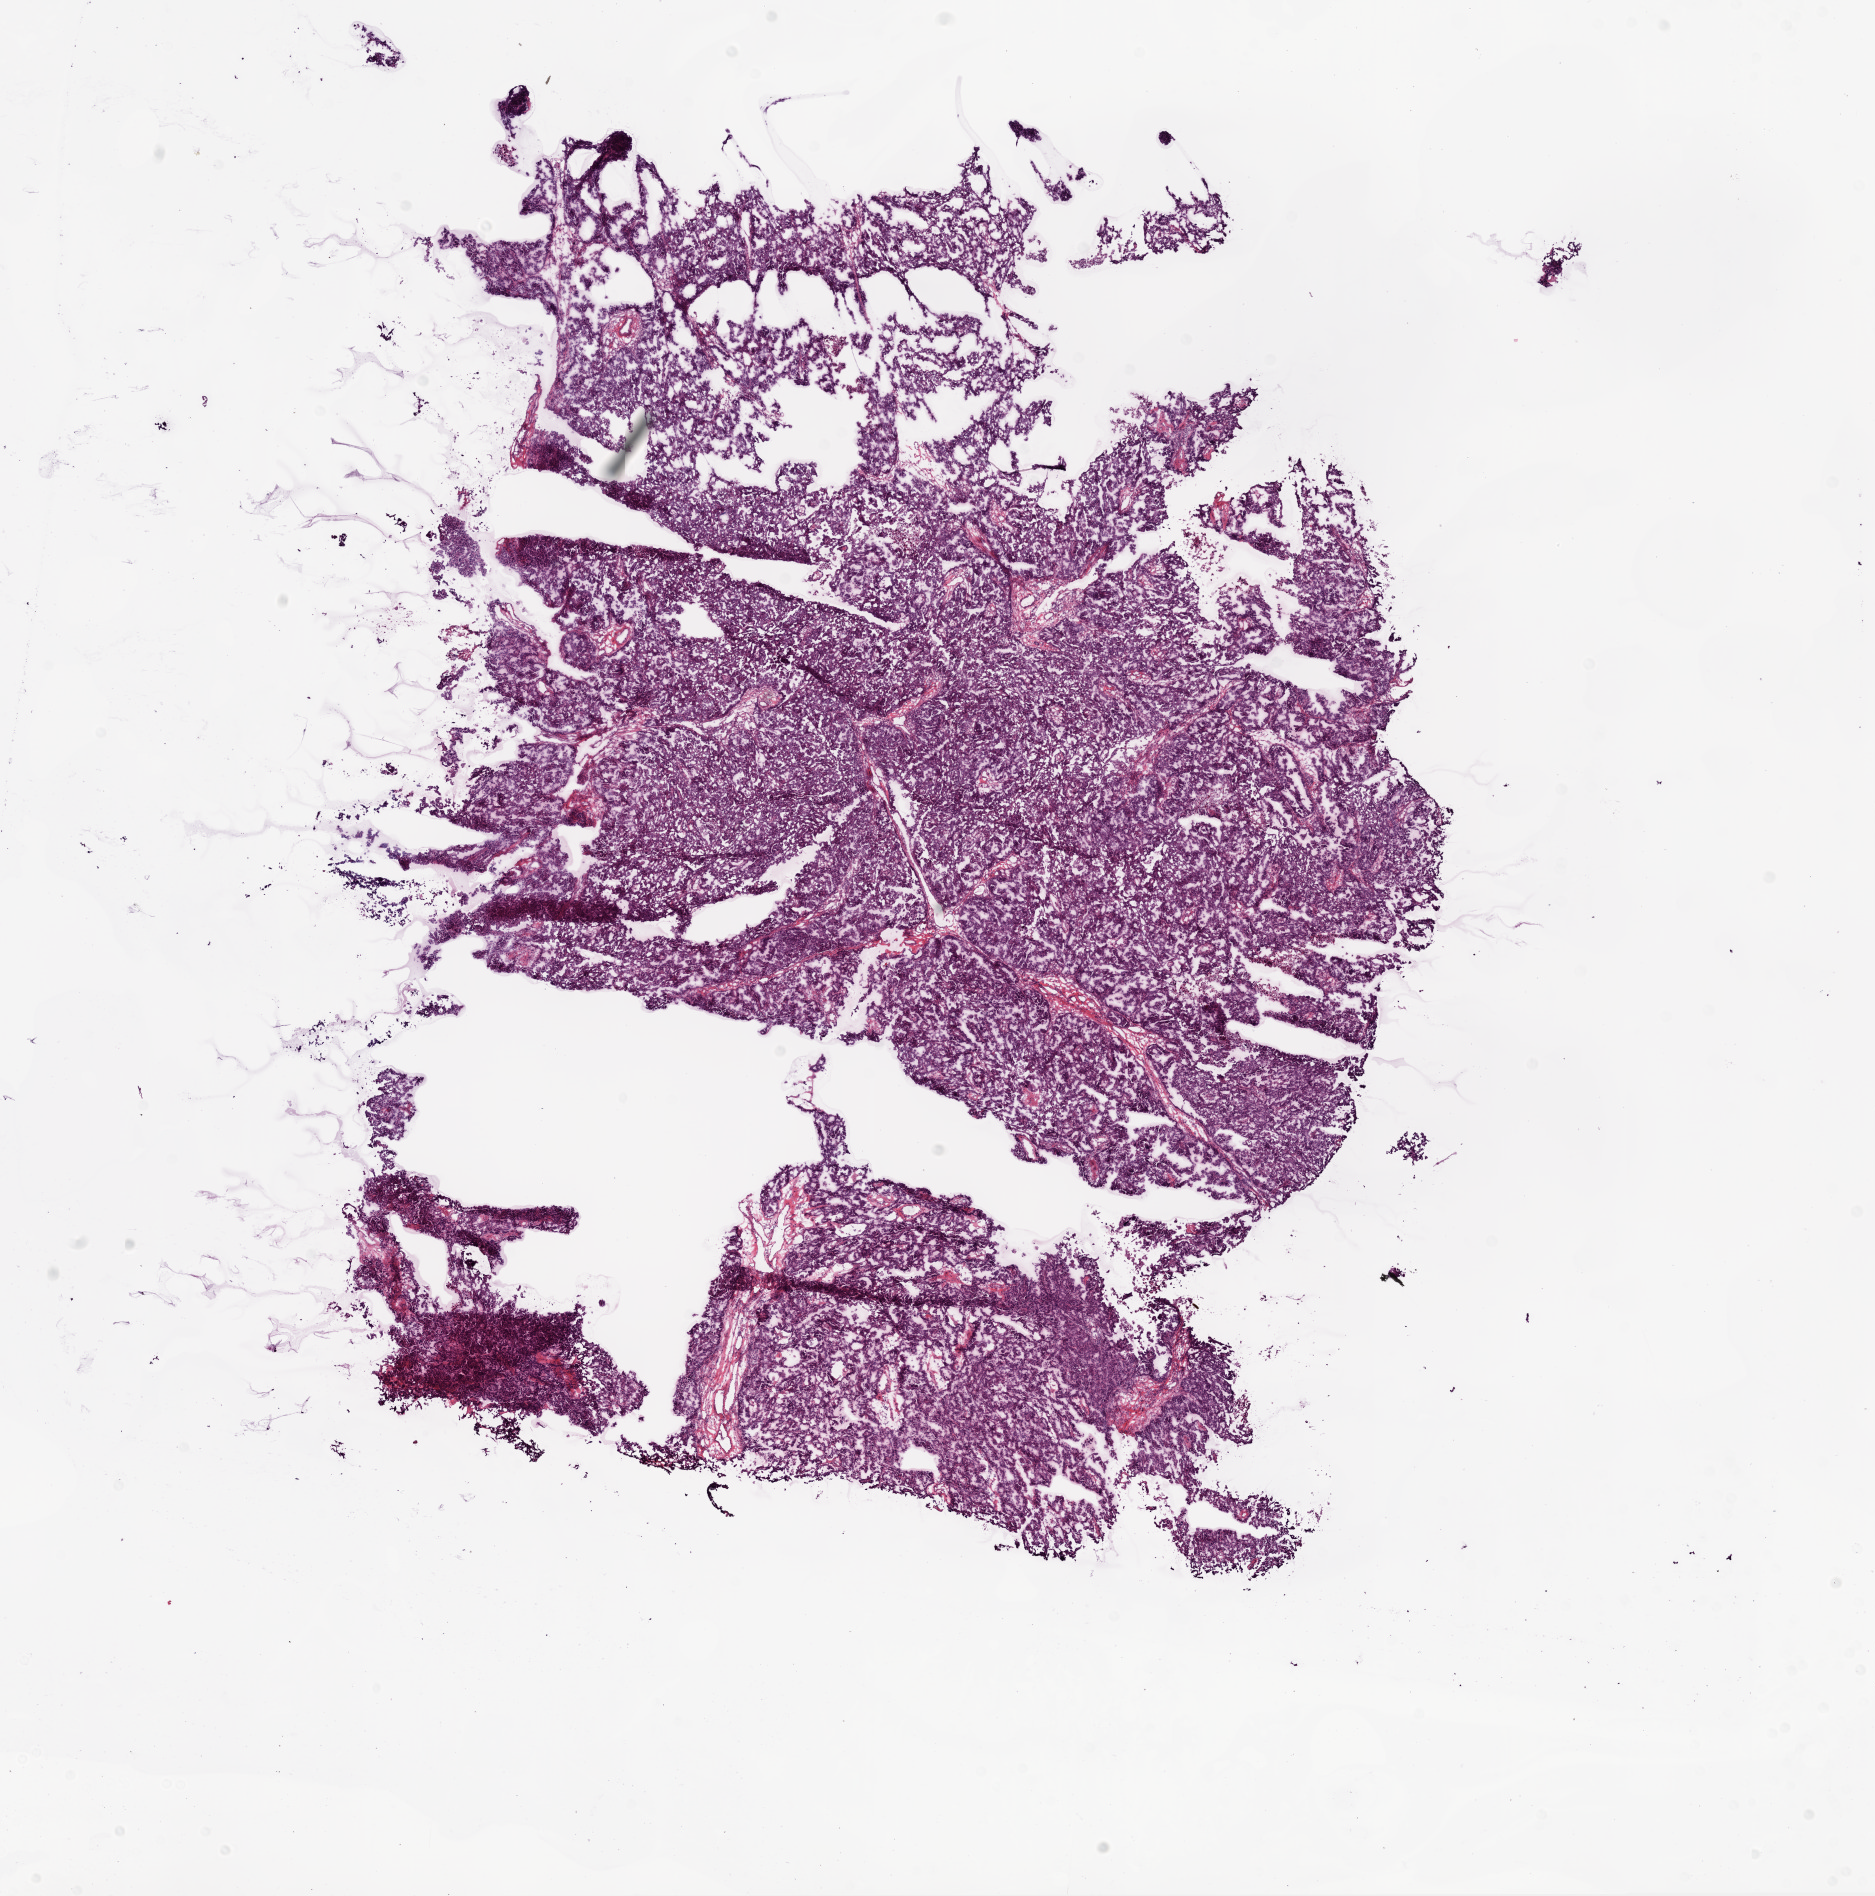
Digitized H&E tissue section (whole slide), low-resolution overview of the scanned area, about 15.0 x 15.2 mm (from a 20x scan). Frozen section from the bottom of the tissue portion. Ovary, primary tumour sample. Female, age 61 years at initial diagnosis.
Pathologic diagnosis: Serous cystadenocarcinoma, NOS.